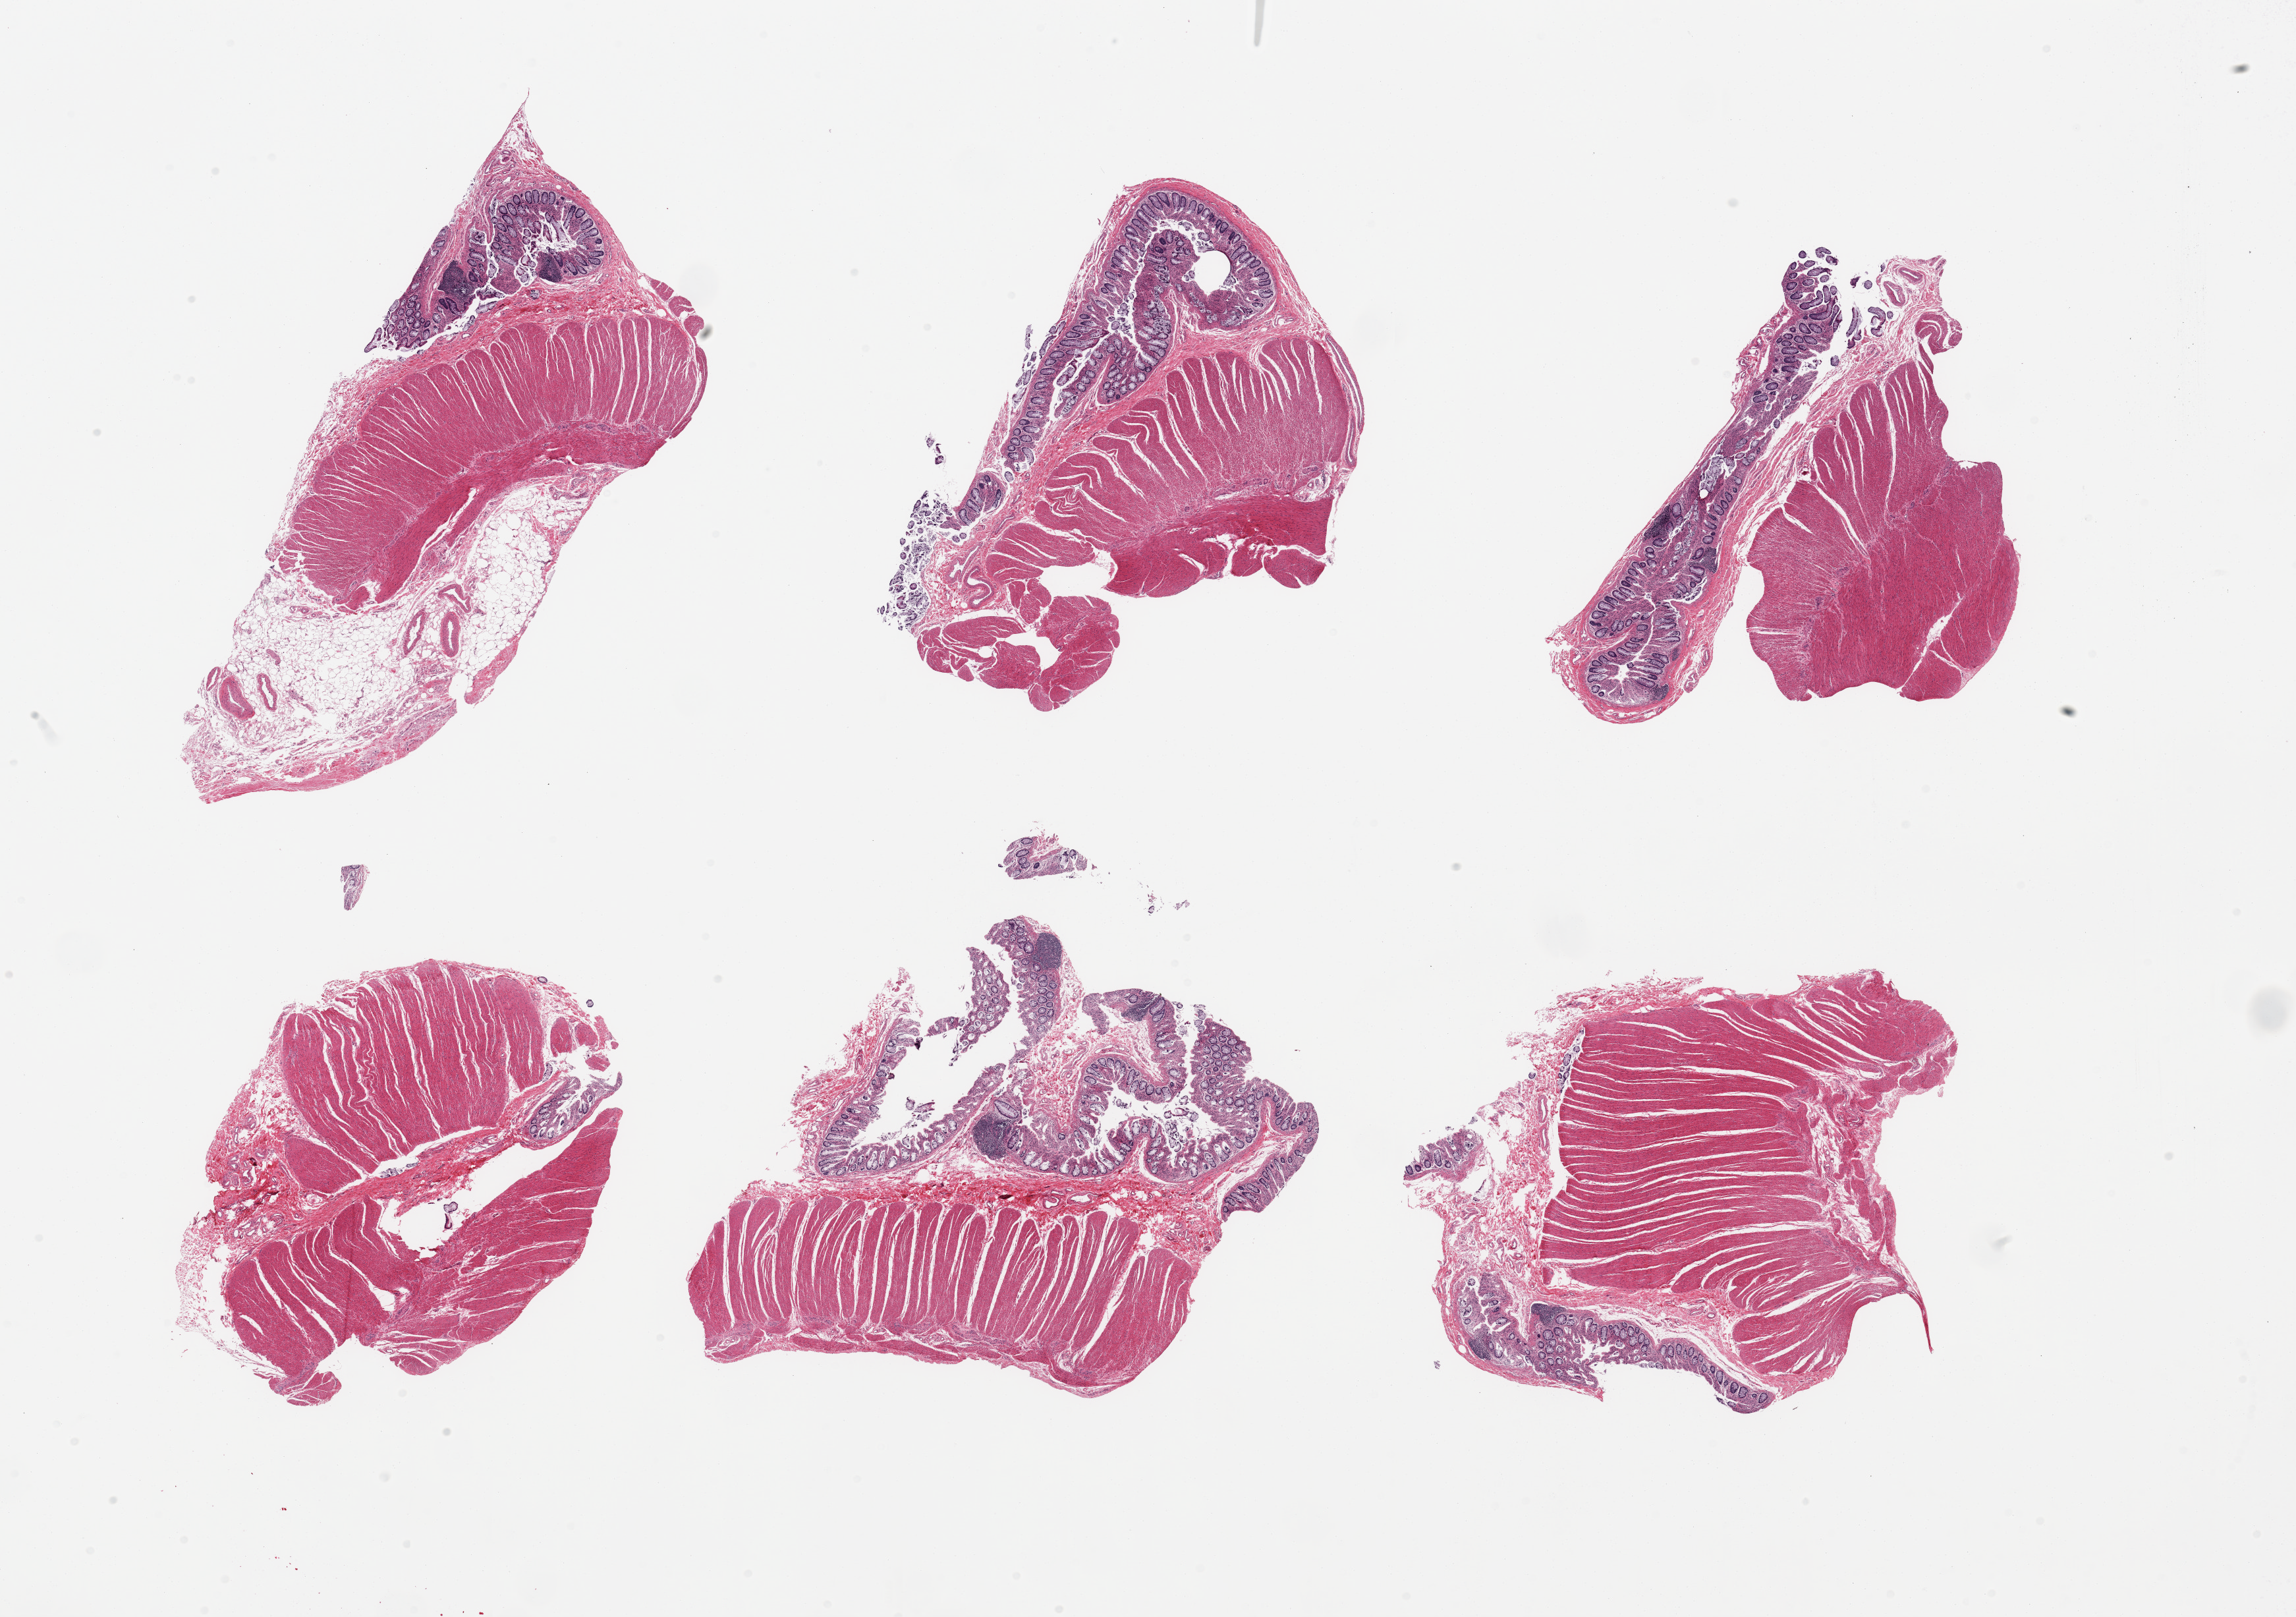
Haematoxylin and eosin whole-slide image — whole scanned area (about 27.6 x 19.4 mm) shown as a low-resolution overview; PAXgene-fixed, paraffin-embedded tissue; section of sigmoid colon (target tissue); donor tissue sample.
• reviewer comment on this tissue sample: 6 pieces, ~20% contaminant mucosa